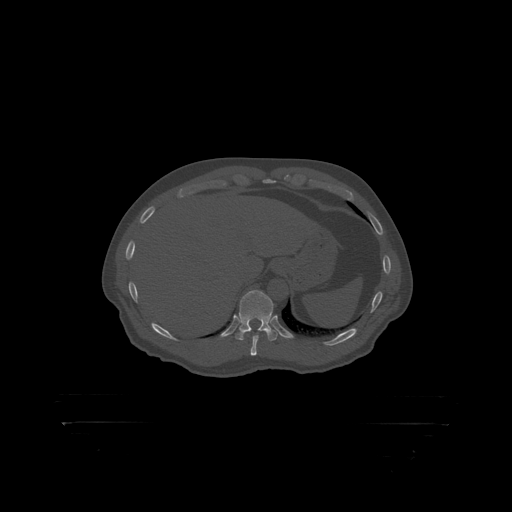
CT including the spine, one axial slice; slice 387 of 399 in the series (ordered by position); bone window (W 1800 / L 400 HU); 1.25 mm slice thickness; 512 × 512 image matrix, field of view 650 × 650 mm. Patient: male, 46 years. Case-level facts recorded for this patient, not image findings: primary cancer: skin.
Annotated regions visible in this slice (semi-automatic segmentation, software-assisted and operator-edited):
- T11 vertebra: bounding box [x1, y1, x2, y2] px = [239, 290, 274, 319]